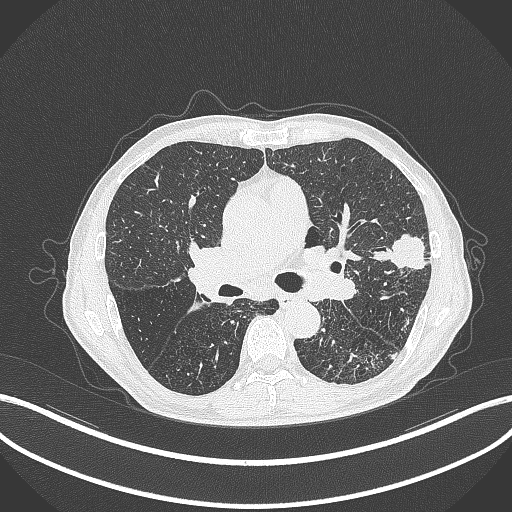
Chest CT, one axial slice. Position 245 of 463 along the scan axis. Reconstruction kernel B70f. Lung window (W 1500 / L -600 HU). 1 mm slice thickness. 512 × 512 image matrix, field of view 400 × 400 mm. Patient: male, 74 years. Case-level facts recorded for this patient, not image findings: clinical TNM (as recorded): T2a N1 M0.
Structures marked on this image (rectangle marked by the reading radiologist):
- lung tumour (recorded histology: adenocarcinoma): bounding box [x1, y1, x2, y2] px = [371, 233, 427, 278]